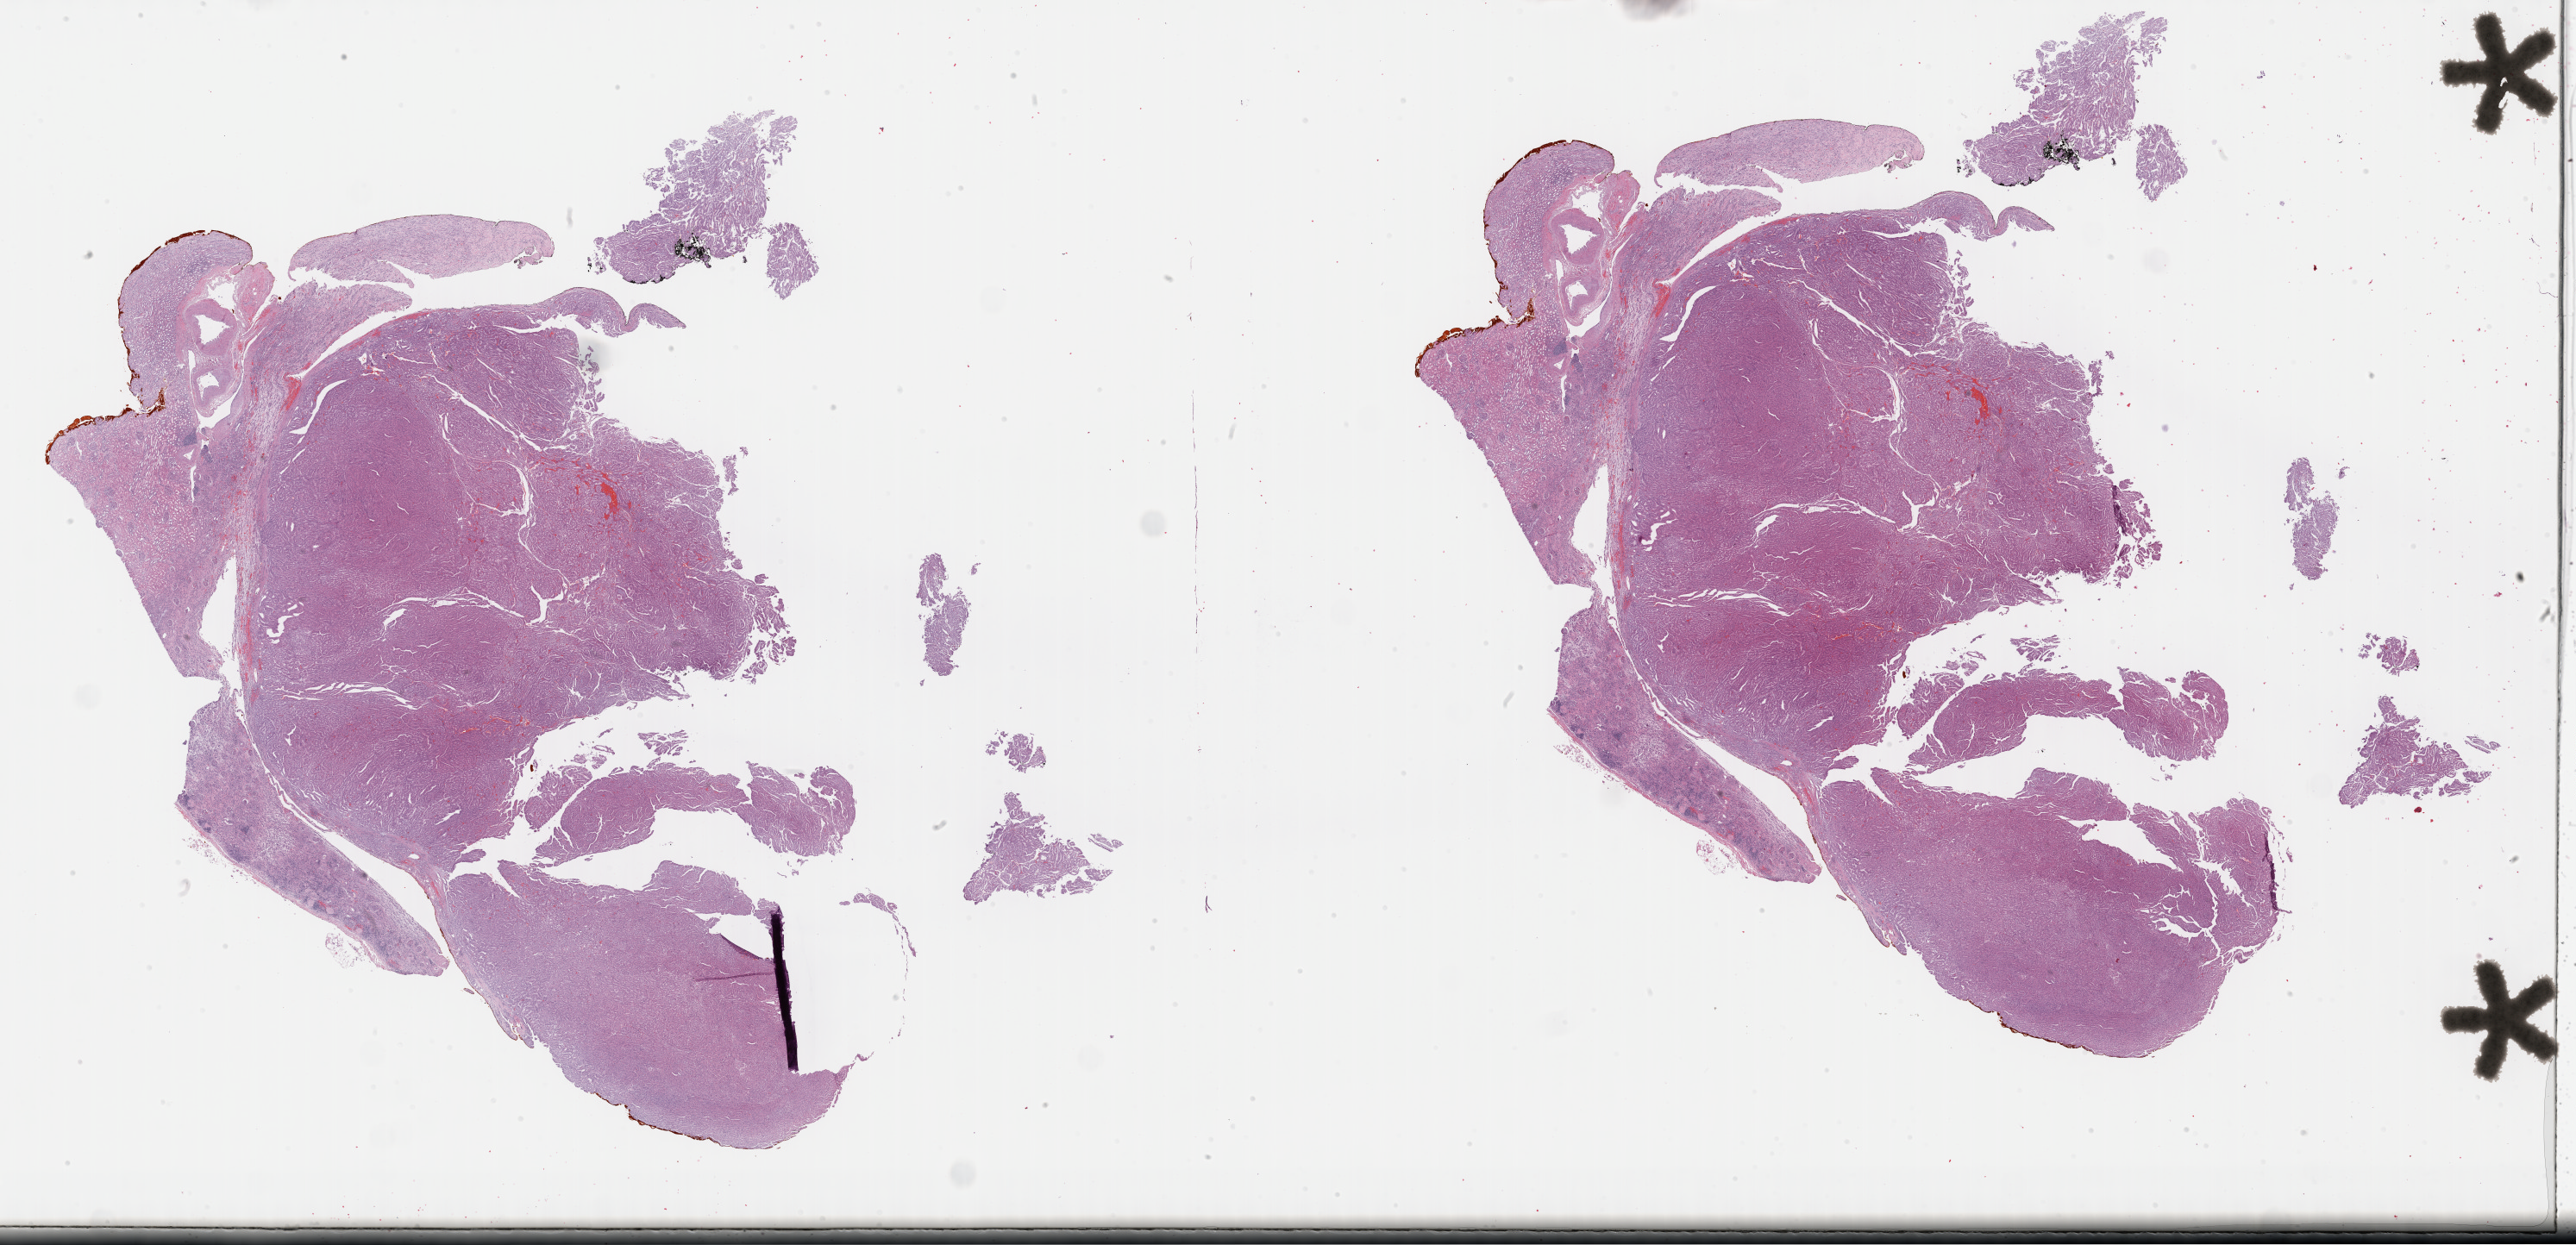
H&E-stained whole-slide image, shown as a low-resolution overview of the whole scanned area (about 48.3 x 23.4 mm), formalin-fixed paraffin-embedded (FFPE) diagnostic section, primary tumour sample from the kidney. Male patient; age at initial diagnosis 61 years.
• AJCC pathologic stage: I (7th edition)
• histologic diagnosis: Papillary adenocarcinoma, NOS
• laterality: right